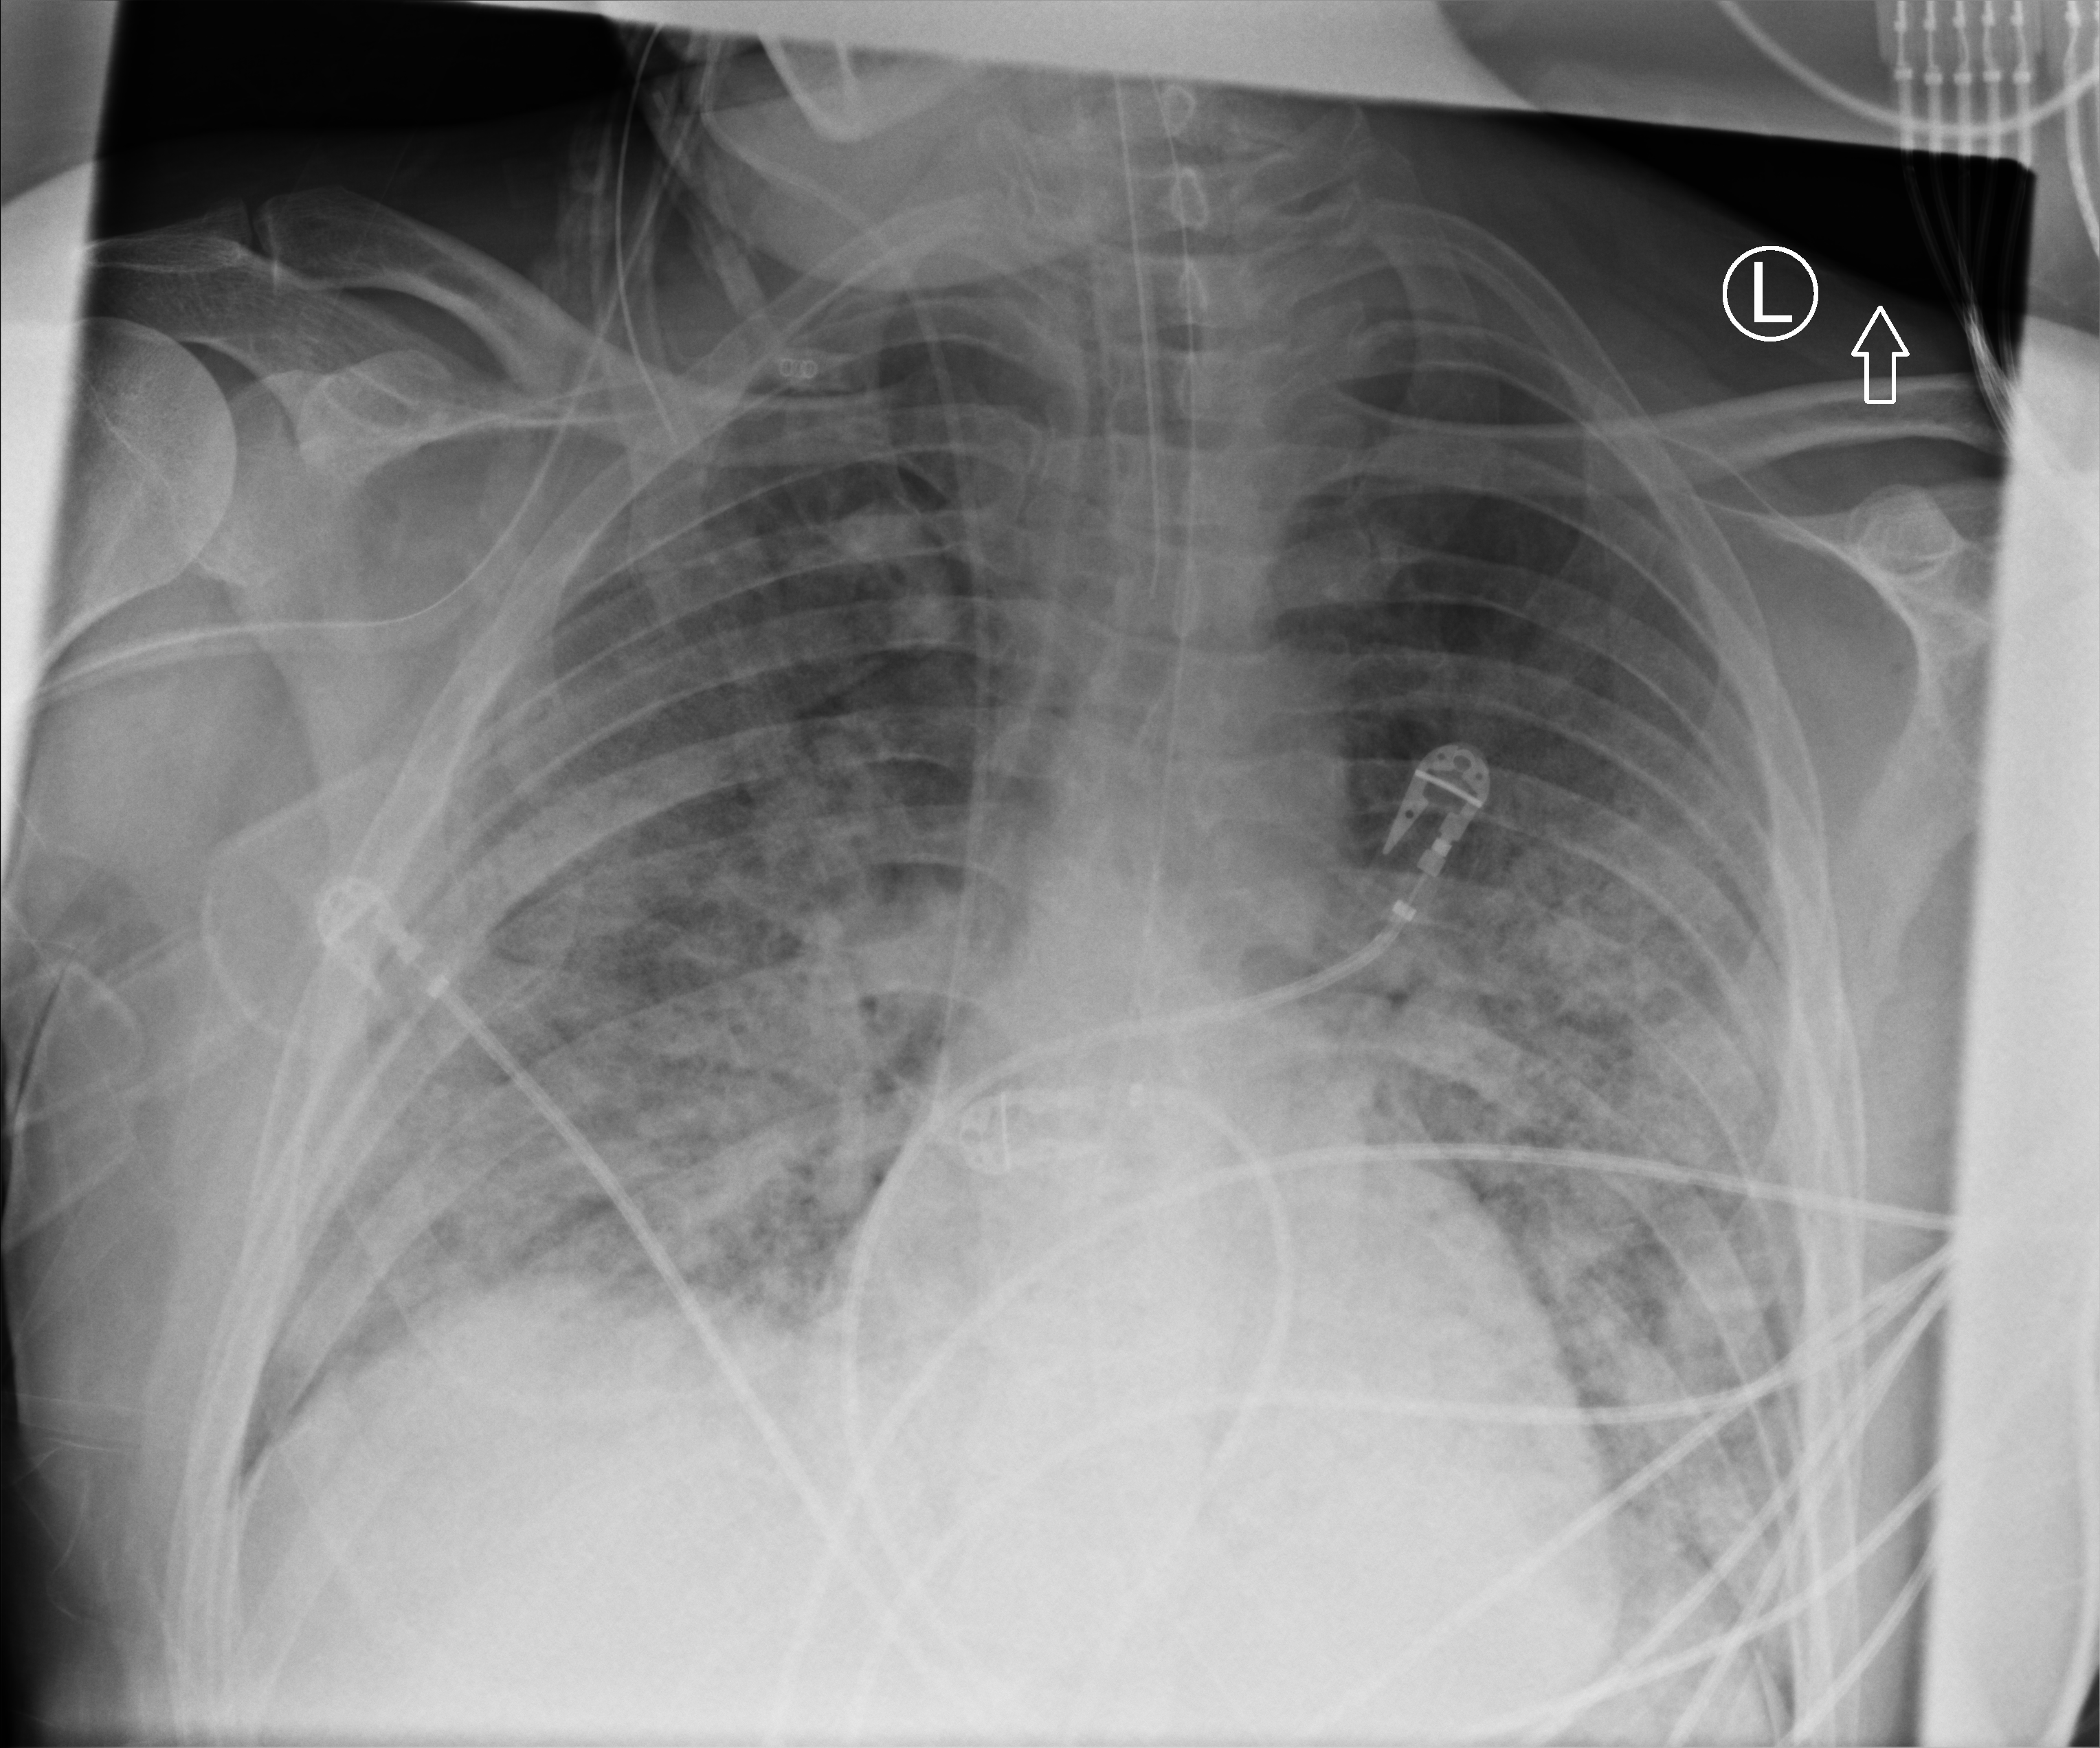
Portable chest radiograph; anteroposterior (AP) projection. Male patient hospitalised with COVID-19, age 18–59 years.
From the hospital-stay record, not from the radiograph (when in the stay this image was taken is not recorded):
- mechanically ventilated during this hospital stay: yes
- admitted to intensive care during this hospital stay: yes
- COPD (admission record): no